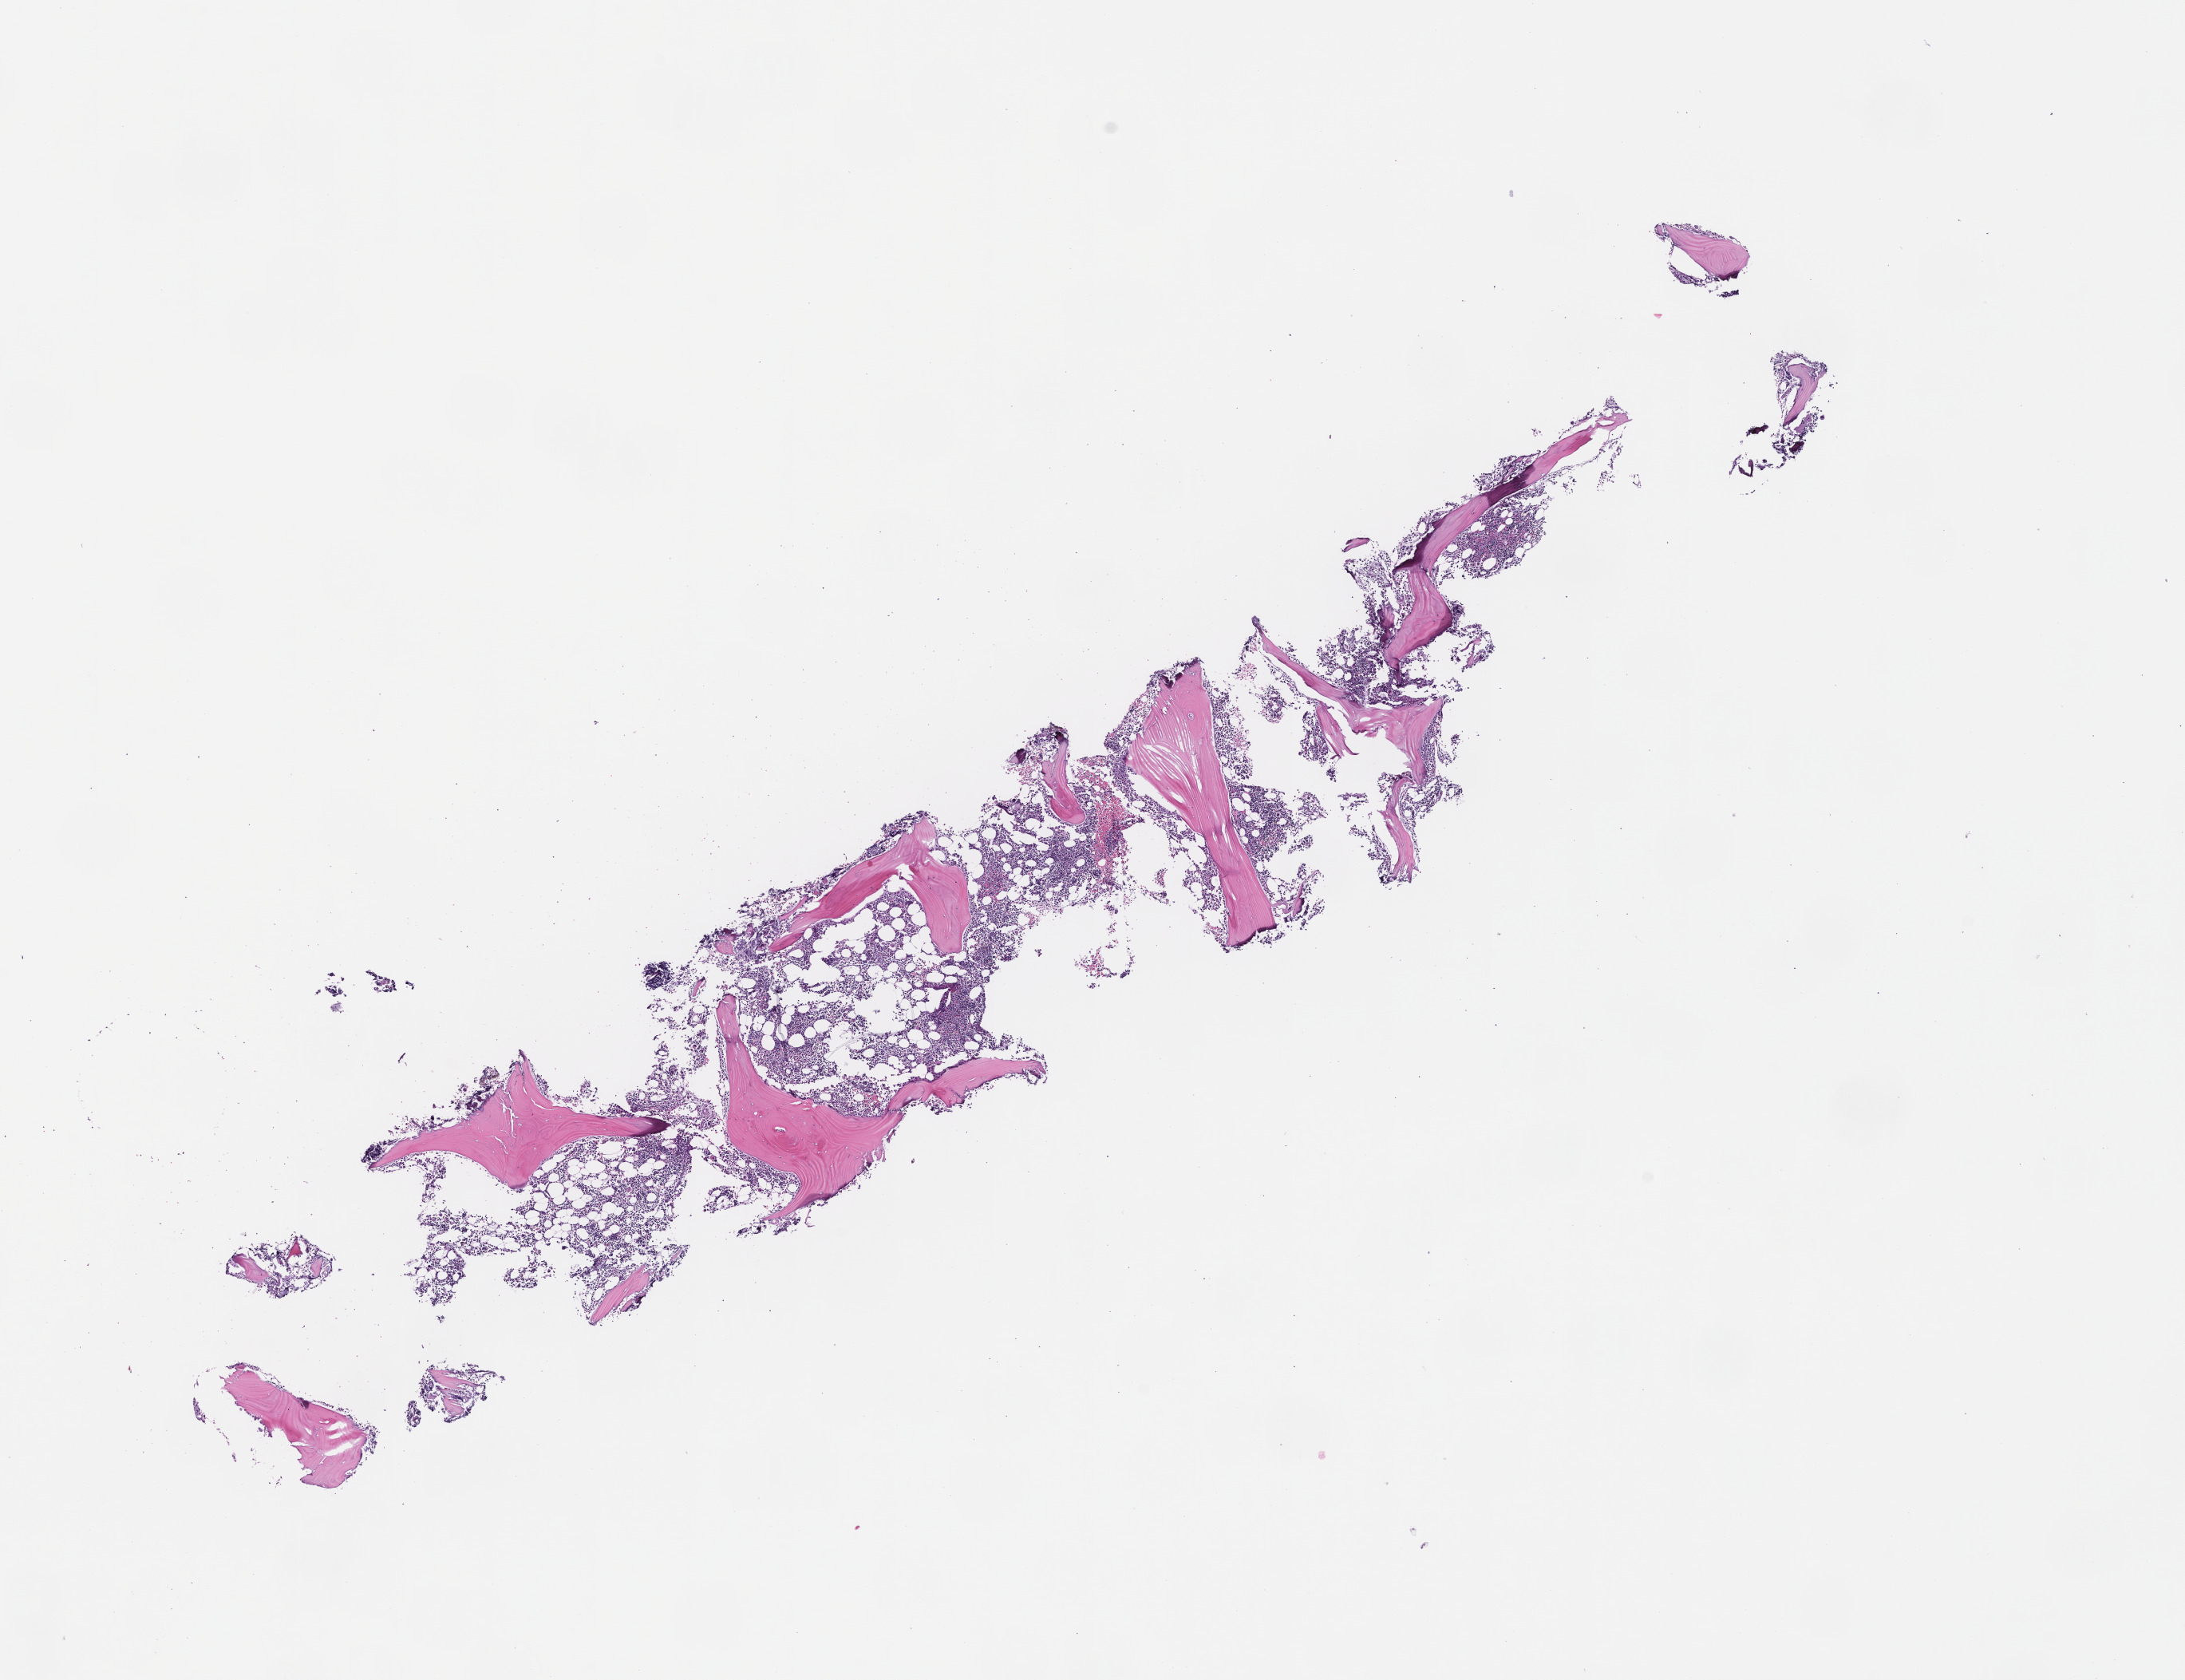
Whole-slide image, H&E stain, low-resolution overview of the scanned area, about 11.1 x 8.5 mm. FFPE section. Site: bone marrow. Collected post-treatment, no progression. Male patient.
• this section: primary tumor
• diagnosis: Acute Myeloid Leukemia Not Otherwise Specified